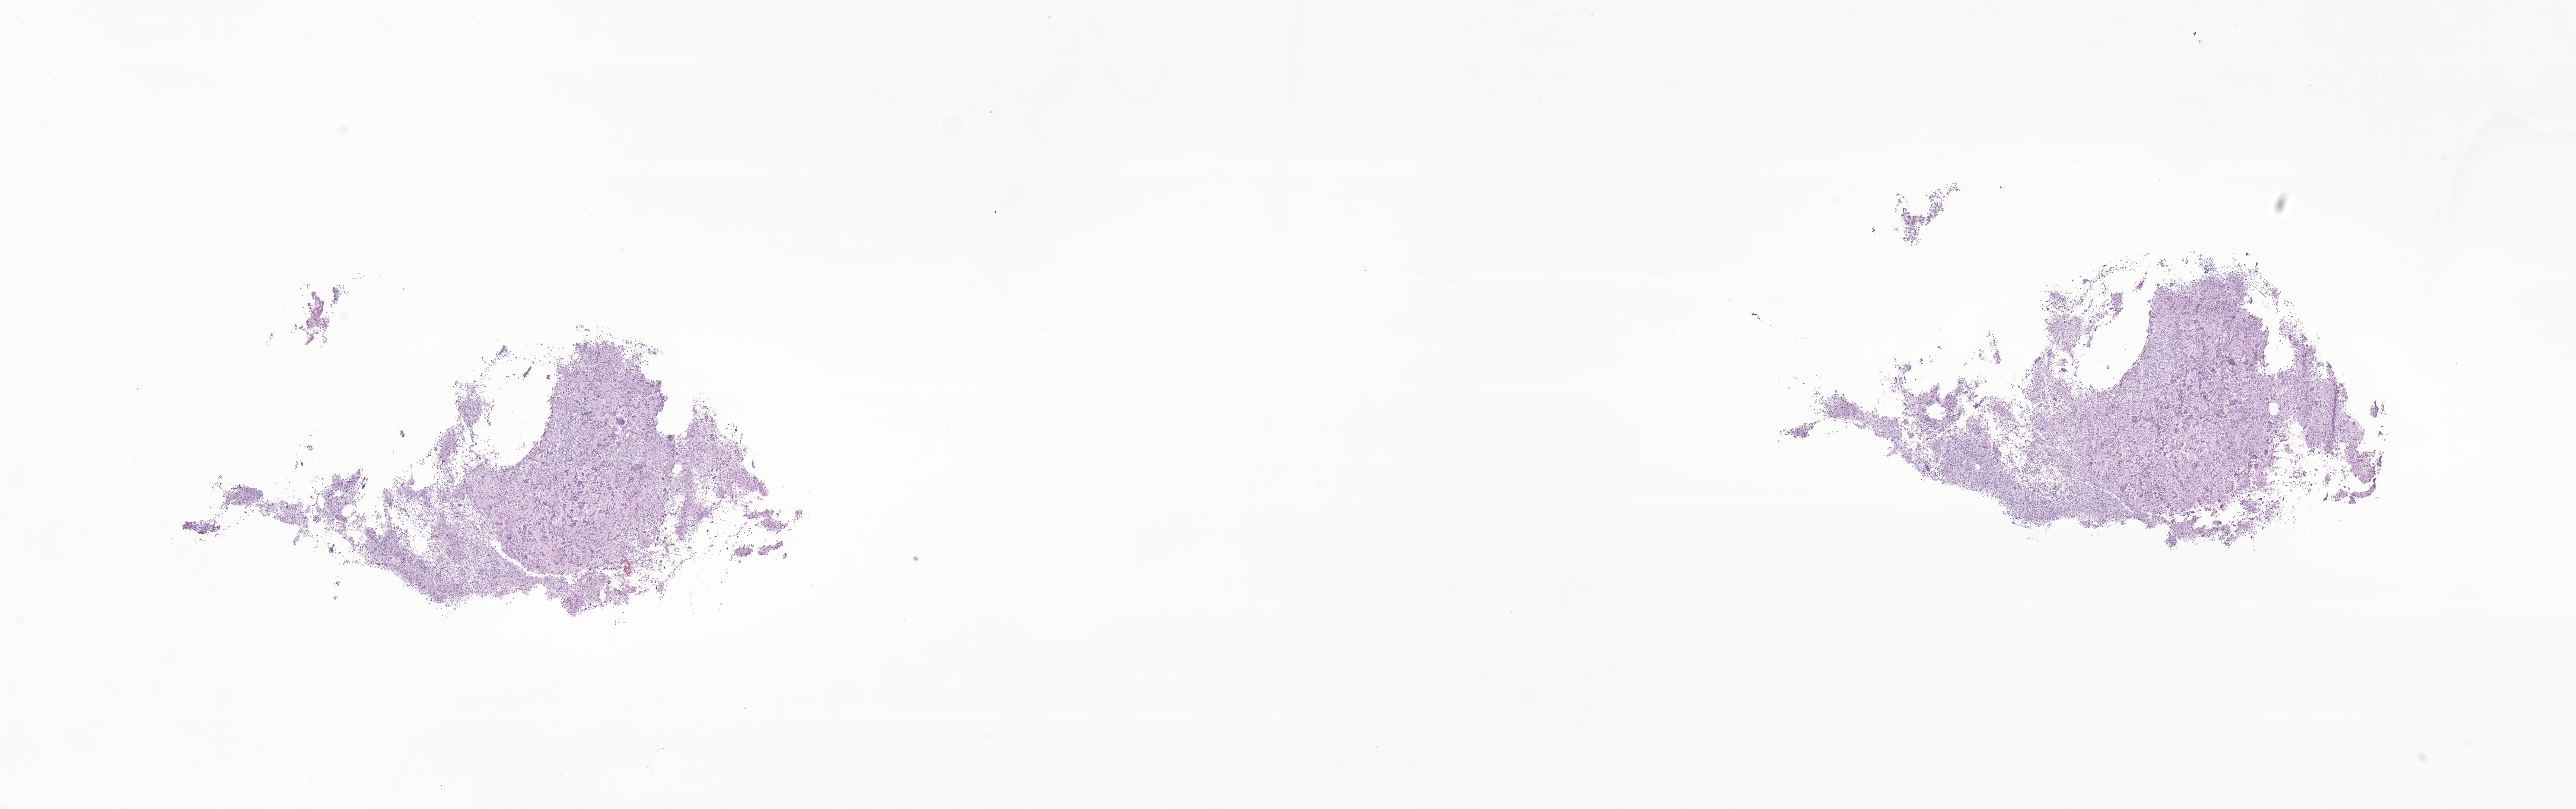
Digitized H&E-stained section of tumor tissue from the cerebral ventricle, shown as a low-resolution overview of the whole scanned area (about 25.1 x 7.9 mm). Frozen section (OCT-embedded). Female patient, age 115 months (9 years 7 months).
Diagnosis: Glioma, malignant.